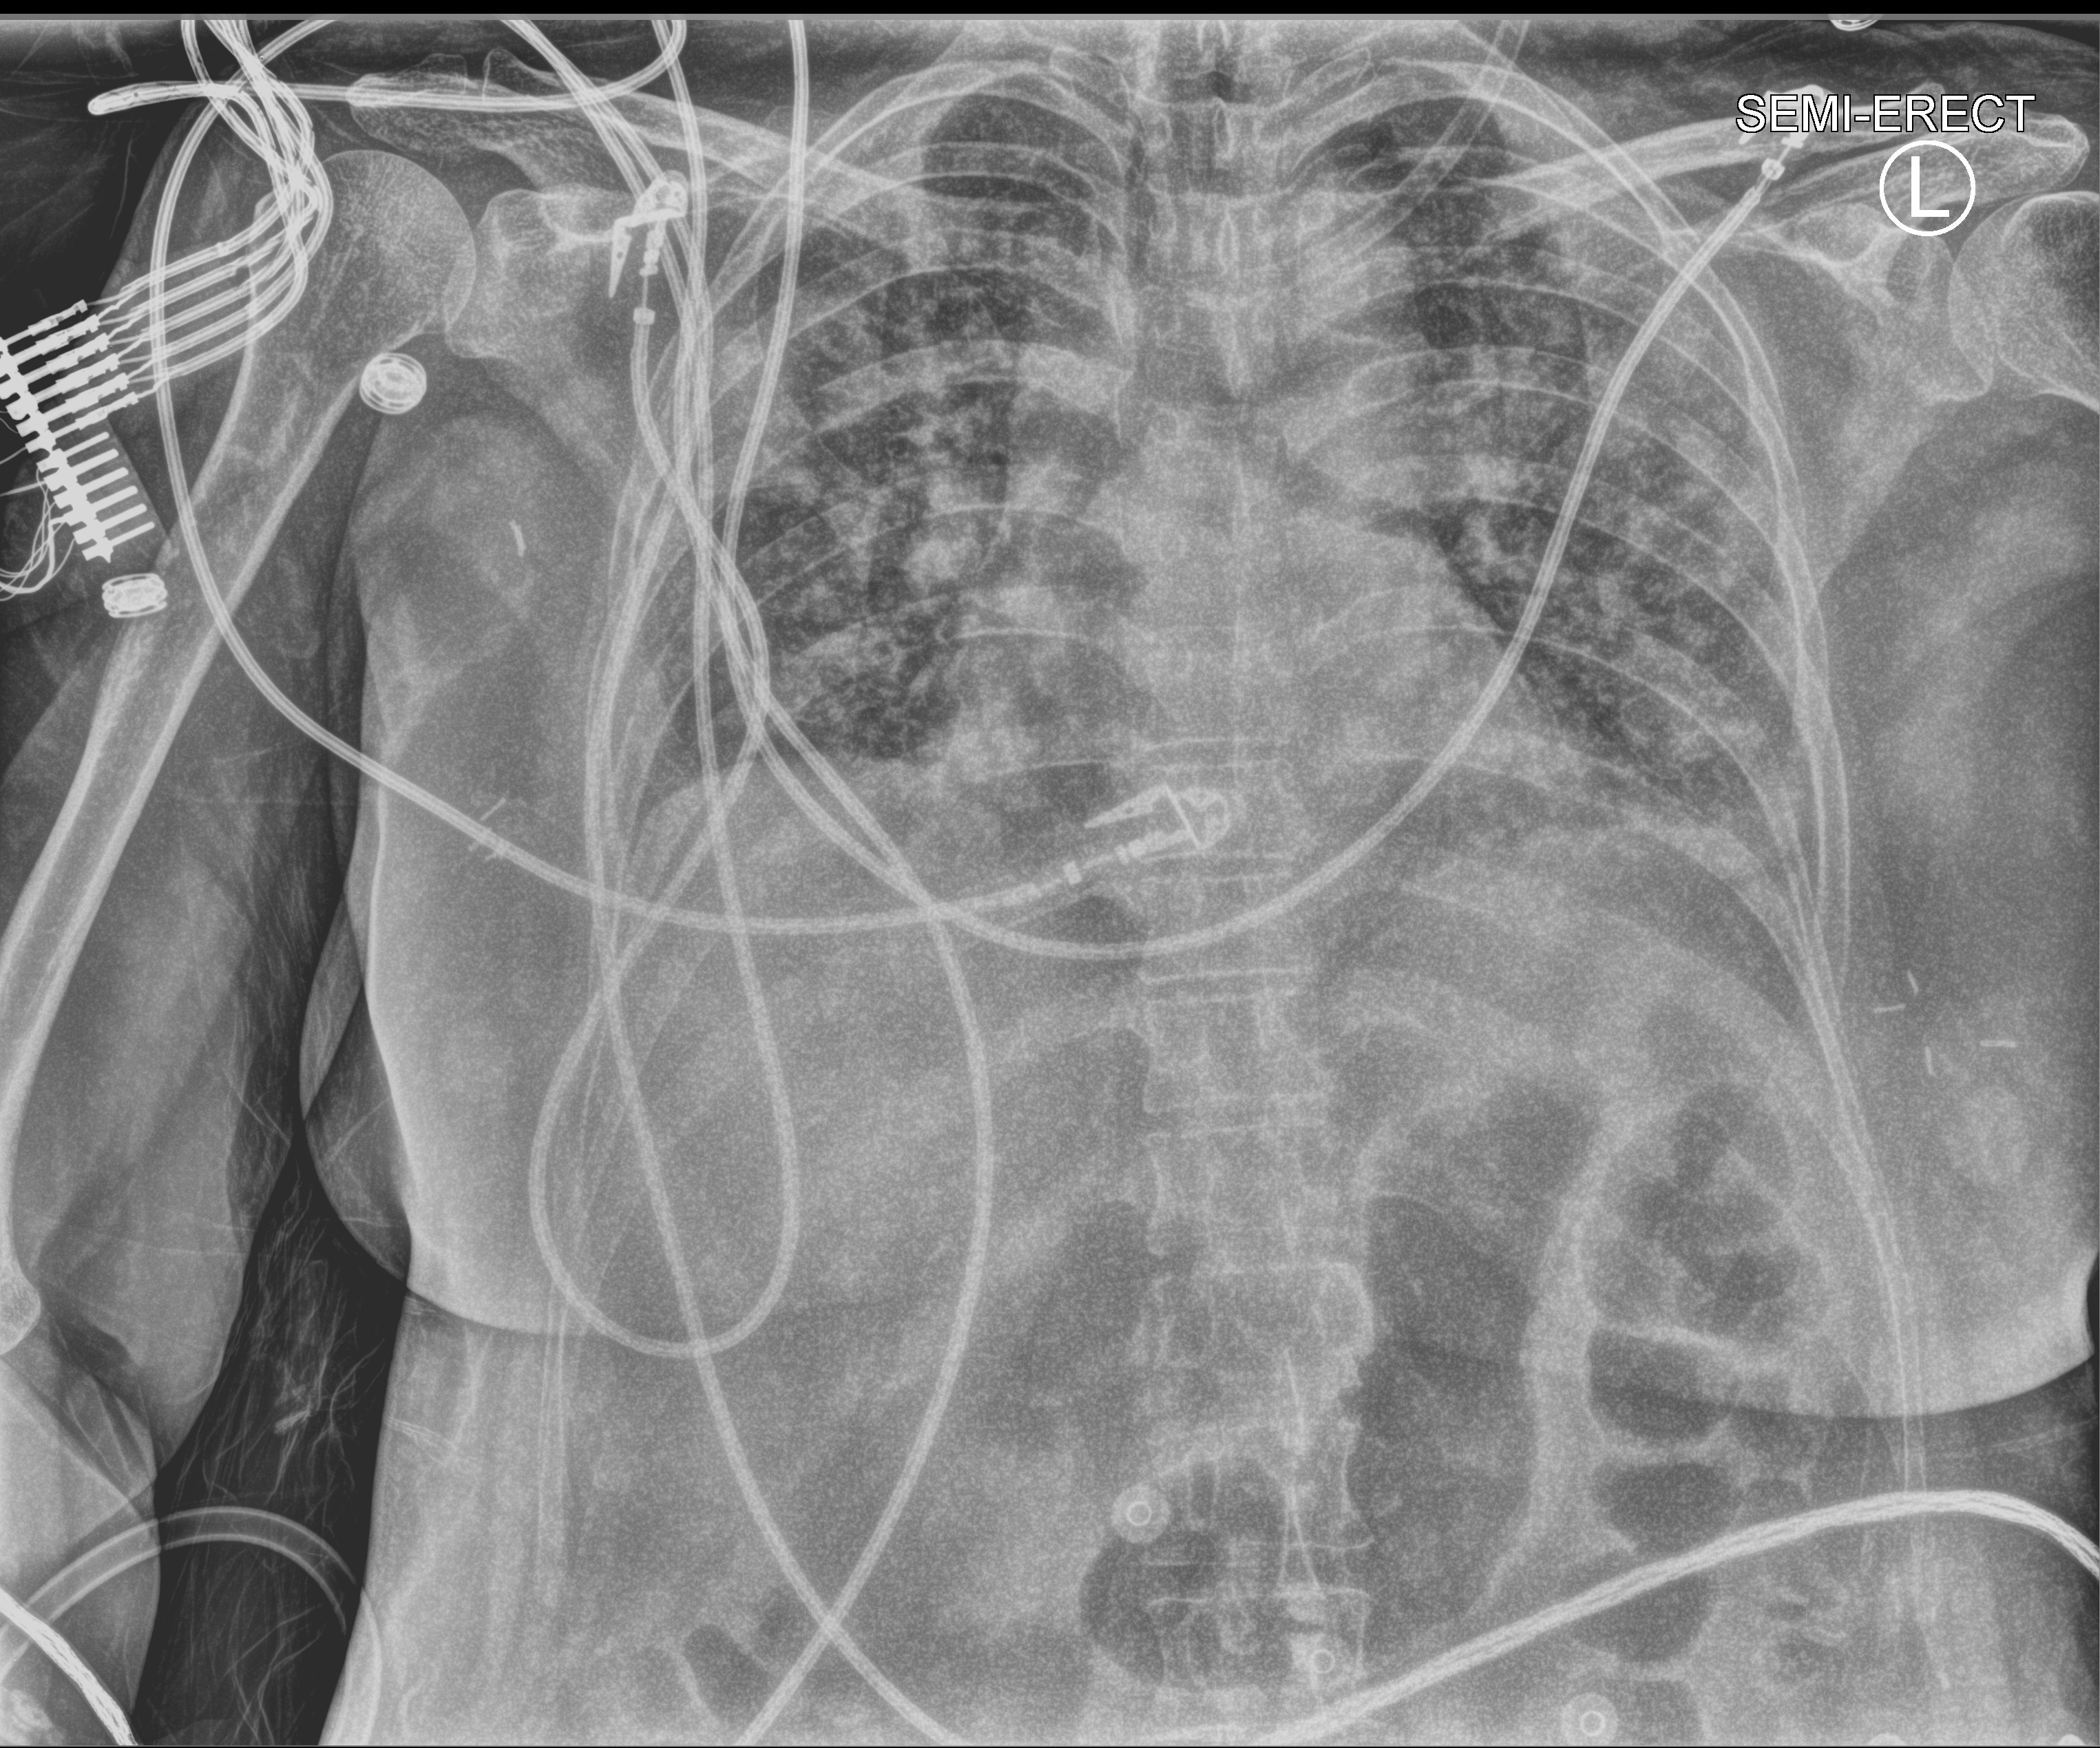
Chest X-ray (portable). Patient hospitalised with COVID-19; female, aged 18–59 years.
Admission-level facts for this patient (not findings on this image; timing relative to this image not recorded): admitted to intensive care during this hospital stay: no; length of hospital stay: 21 days.